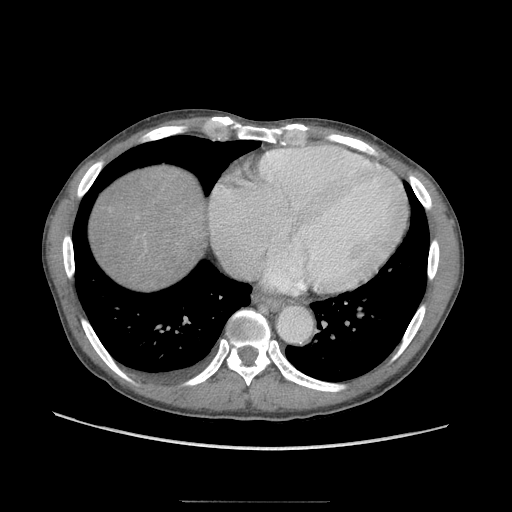
Contrast-enhanced abdominal CT (liver protocol), one axial slice. Slice 95 of 103 in the series (ordered by position). Reconstruction kernel STANDARD. Soft-tissue window (W 400 / L 40 HU). 2.5 mm slice thickness. 512 × 512 image matrix, field of view 380 × 380 mm. Case-level facts recorded for this patient, not image findings: diagnosis: hepatocellular carcinoma (patient treated with transarterial chemoembolisation; whether this scan precedes or follows treatment is not stated here); TNM stage (as recorded): Stage-IIIA; Child-Pugh class: A; tumour differentiation: moderately differentiated; tumour nodularity: multinodular.
Structures marked on this image (semi-automatic segmentation, software-assisted and operator-edited):
- abdominal aorta: bounding box [x1, y1, x2, y2] px = [278, 306, 311, 342]
- liver parenchyma outside the tumour (the mass and vessels are separate outlines, so this box may not span the whole liver): [92, 167, 202, 282]